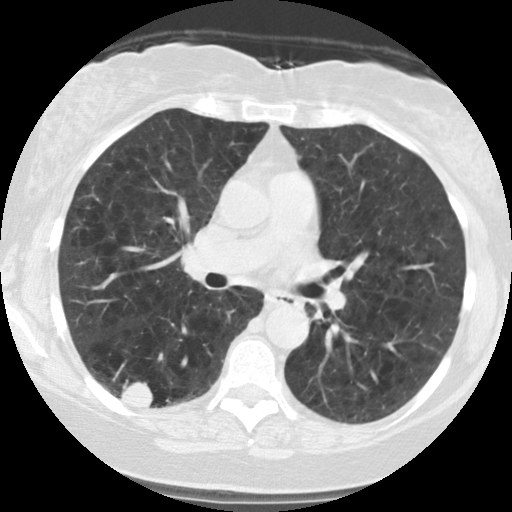
Low-dose screening chest CT, one axial slice. Position 65 of 122 along the scan axis. 140 kVp. Lung window (W 1500 / L -600 HU). 512 × 512 image matrix, field of view 310 × 310 mm.
Structures marked on this image (manually delineated by an expert):
- lesion 1 (tumor, lower lobe of right lung): bounding box <121,381,153,406> (left, top, right, bottom; pixels)